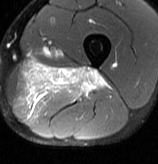
MRI of an extremity soft-tissue mass, one axial slice; T2-weighted fat-saturated; MR volume resampled by the dataset authors to the PET/CT grid (not the native acquisition matrix); 158 × 164 image matrix, field of view 154 × 160 mm. Male patient. Case-level facts recorded for this patient, not image findings: histological type: extraskeletal osteosarcoma; grade: high; site of the primary tumour: left adductur.
Outlined on this slice (expert contour drawn on MRI and transferred to this co-registered scan by the dataset authors):
- gross tumour volume (mass): bounding box <15,60,110,120> (left, top, right, bottom; pixels)